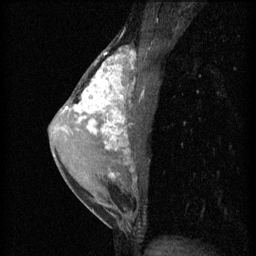
Breast MRI (dynamic contrast-enhanced), one sagittal slice. Slice 31 of 60 in the series (ordered by position). 3 images stored at this slice position (order not interpretable as contrast timing). 1.5 T. TE 4.2 ms, TR 11 ms. 2 mm slice thickness. 256 × 256 image matrix, field of view 180 × 180 mm. Female patient, age 40 years.
Structures marked on this image (semi-automatic segmentation, software-assisted and operator-edited):
- analysis volume of interest (the breast-tissue region the enhancement analysis was run in; not a lesion): box from (x=55, y=44) to (x=143, y=203) px
- tumour enhancement mask (voxels above the 70 % enhancement threshold inside the analysis volume of interest): (x=63, y=48)–(x=136, y=177)